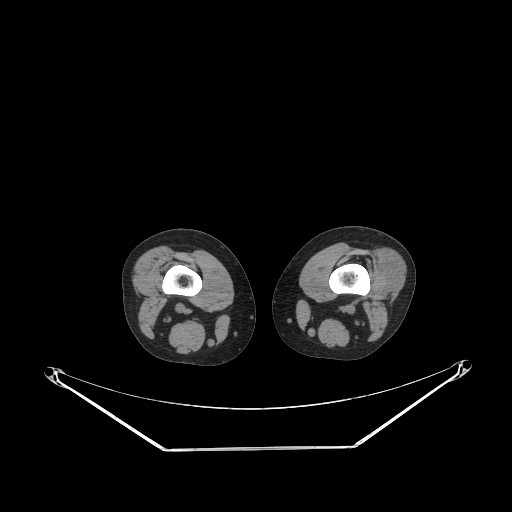
CT of an extremity soft-tissue mass (from a PET/CT study), one axial slice; slice 177 of 223 in the series (ordered by position); reconstruction kernel STANDARD; 140 kVp; soft-tissue window (W 400 / L 40 HU); 3.75 mm slice thickness; 512 × 512 image matrix. Female patient. From the clinical record (not read from this slice): histological type: spindle cell suggestive of biphasic synovial sarcoma; grade: intermediate; site of the primary tumour: left knee.
Structures marked on this image (expert contour drawn on MRI and transferred to this co-registered scan by the dataset authors):
- gross tumour volume including surrounding oedema: bounding box [x1, y1, x2, y2] px = [377, 246, 405, 295]
- gross tumour volume (mass): [377, 247, 405, 295]